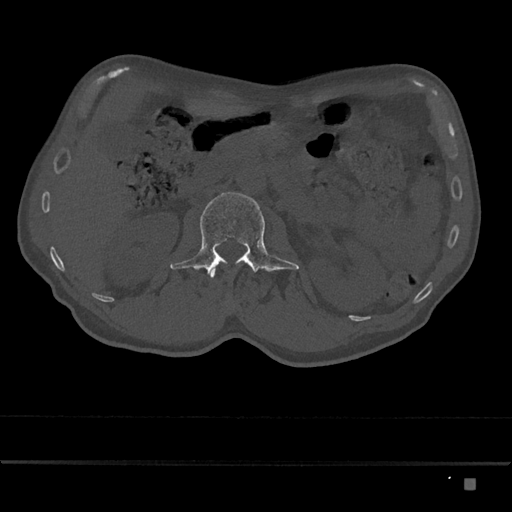
CT including the spine, one axial slice. Slice 487 of 797 in the series (ordered by position). 120 kVp. Bone window (W 1800 / L 400 HU). 0.5 mm slice thickness. 512 × 512 image matrix. Patient: male, 72 years. From the clinical record (not read from this slice): primary cancer: prostate.
Structures marked on this image (semi-automatic segmentation, software-assisted and operator-edited):
- L1 vertebra: bounding box <210,269,216,278> (left, top, right, bottom; pixels)
- L2 vertebra: <170,192,299,275>